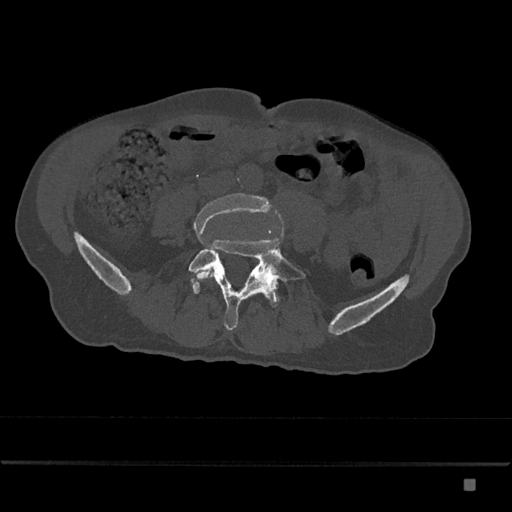
CT including the spine, one axial slice; reconstruction kernel Br40s/3; 120 kVp; bone window (W 1800 / L 400 HU); 0.5 mm slice thickness; 512 × 512 image matrix, field of view 390 × 390 mm. Patient: male, 72 years. From the clinical record (not read from this slice): primary cancer: prostate.
Annotated regions visible in this slice (semi-automatic segmentation, software-assisted and operator-edited):
- L4 vertebra: bounding box <193,193,273,280> (left, top, right, bottom; pixels)
- L5 vertebra: <188,238,306,330>